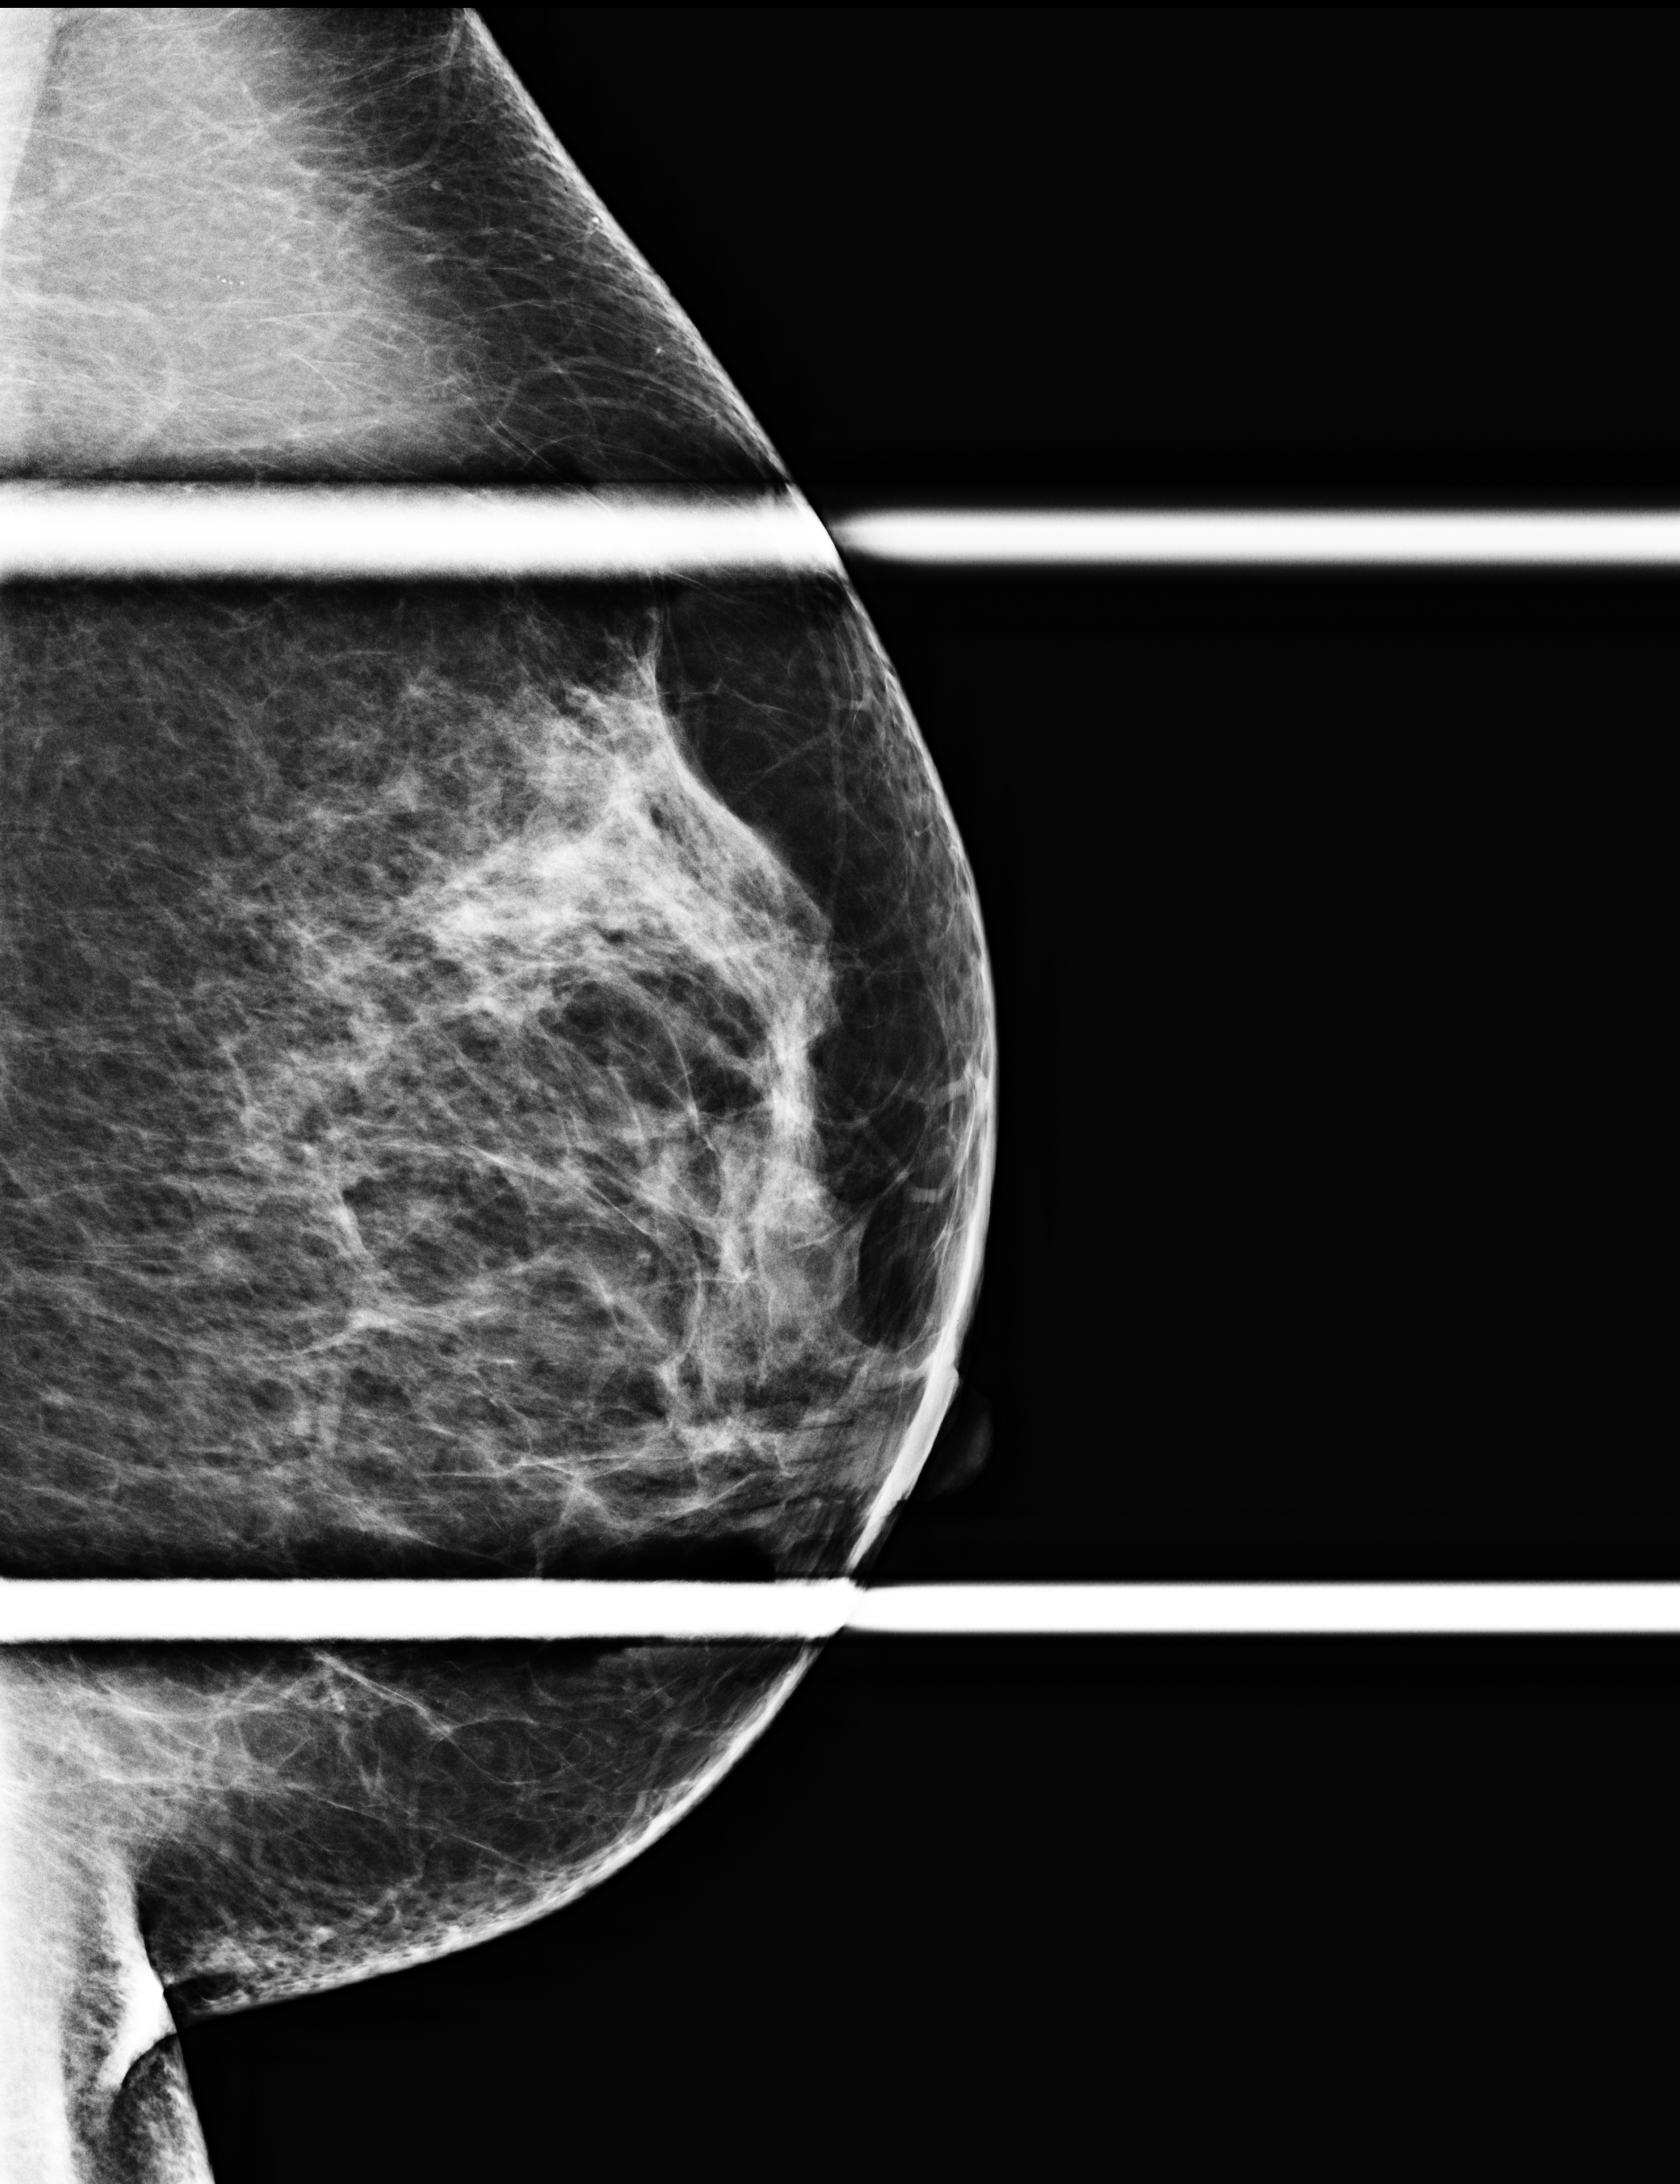
Full-field digital mammogram (FFDM), left breast, ML view (spot compression), additional work-up view, compressed breast thickness 59 mm. Female patient, age 56 years.
BI-RADS breast density category at the screening exam (both breasts, scale 1–4): 3. Final BI-RADS category for the screening round (tomosynthesis exam, both breasts): category 1. Recall: recalled for additional imaging after this screen.